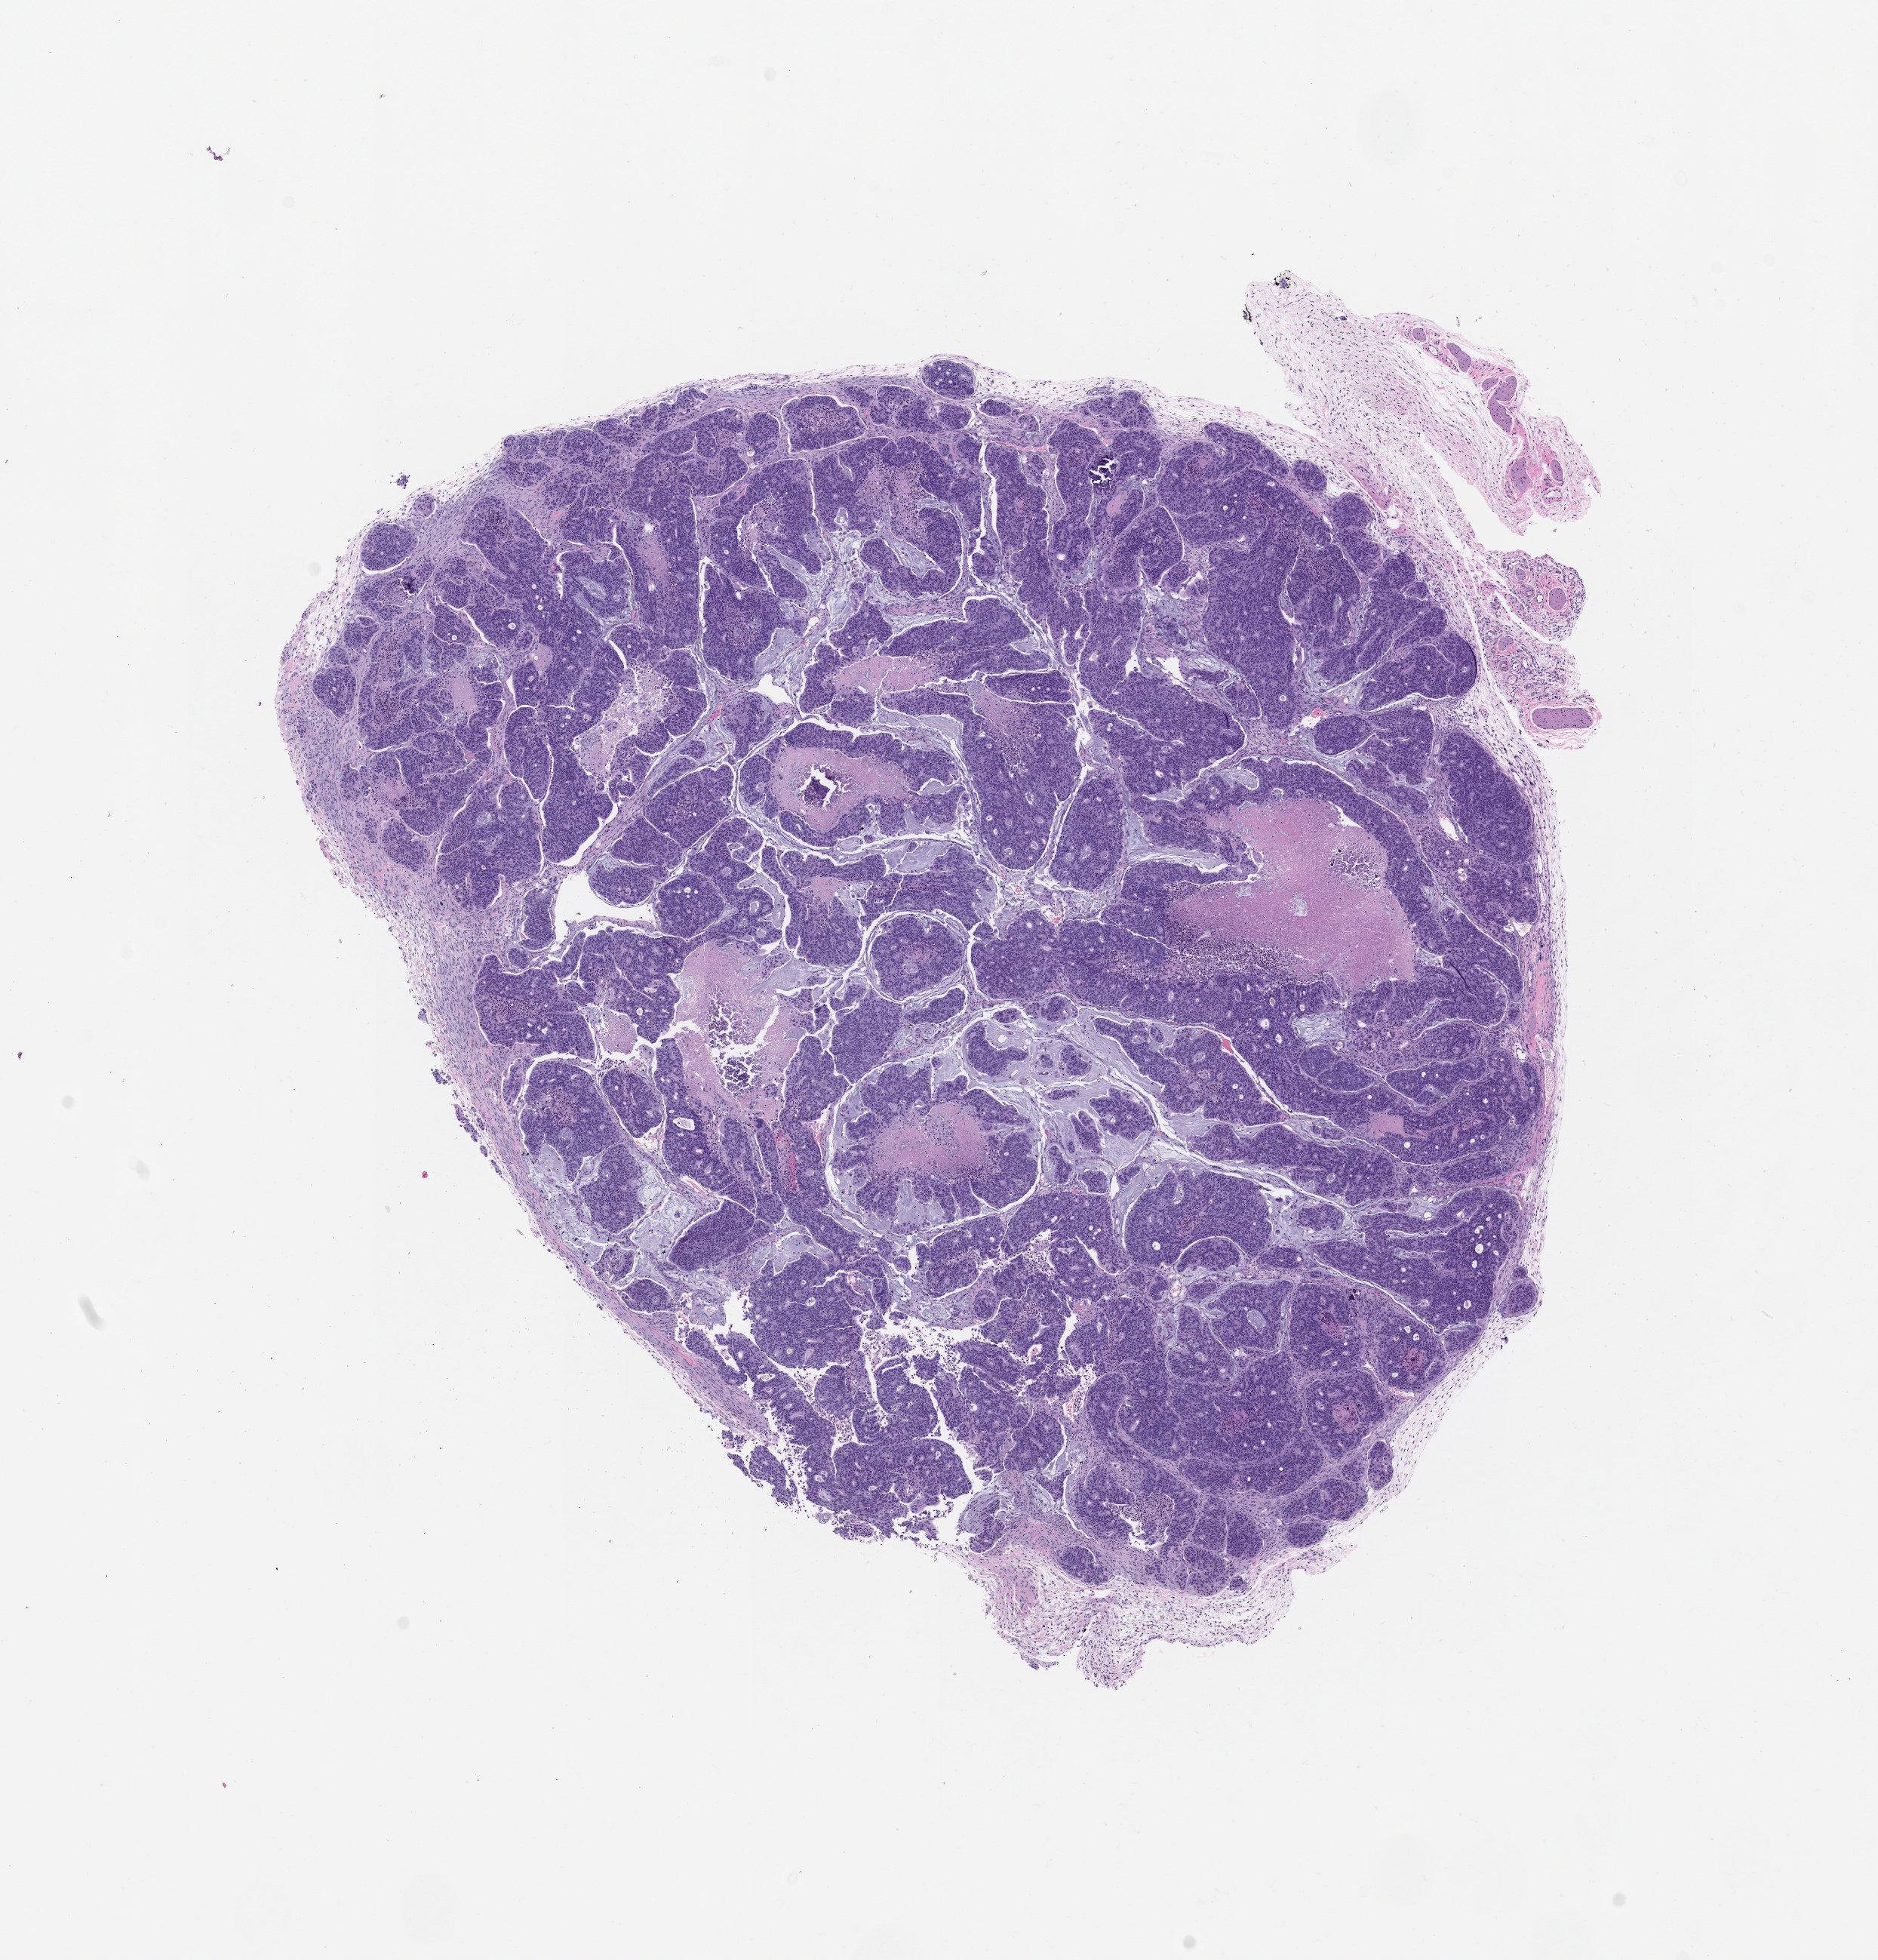
Whole-slide image, hematoxylin and eosin (H&E): patient-derived xenograft (human tumor grown in a mouse), passage 2, low-resolution overview of the scanned area, about 10.0 x 10.4 mm, formalin-fixed, paraffin-embedded (FFPE) tissue, originating tumor site category: colon.
• originating patient diagnosis: Colon Adenocarcinoma